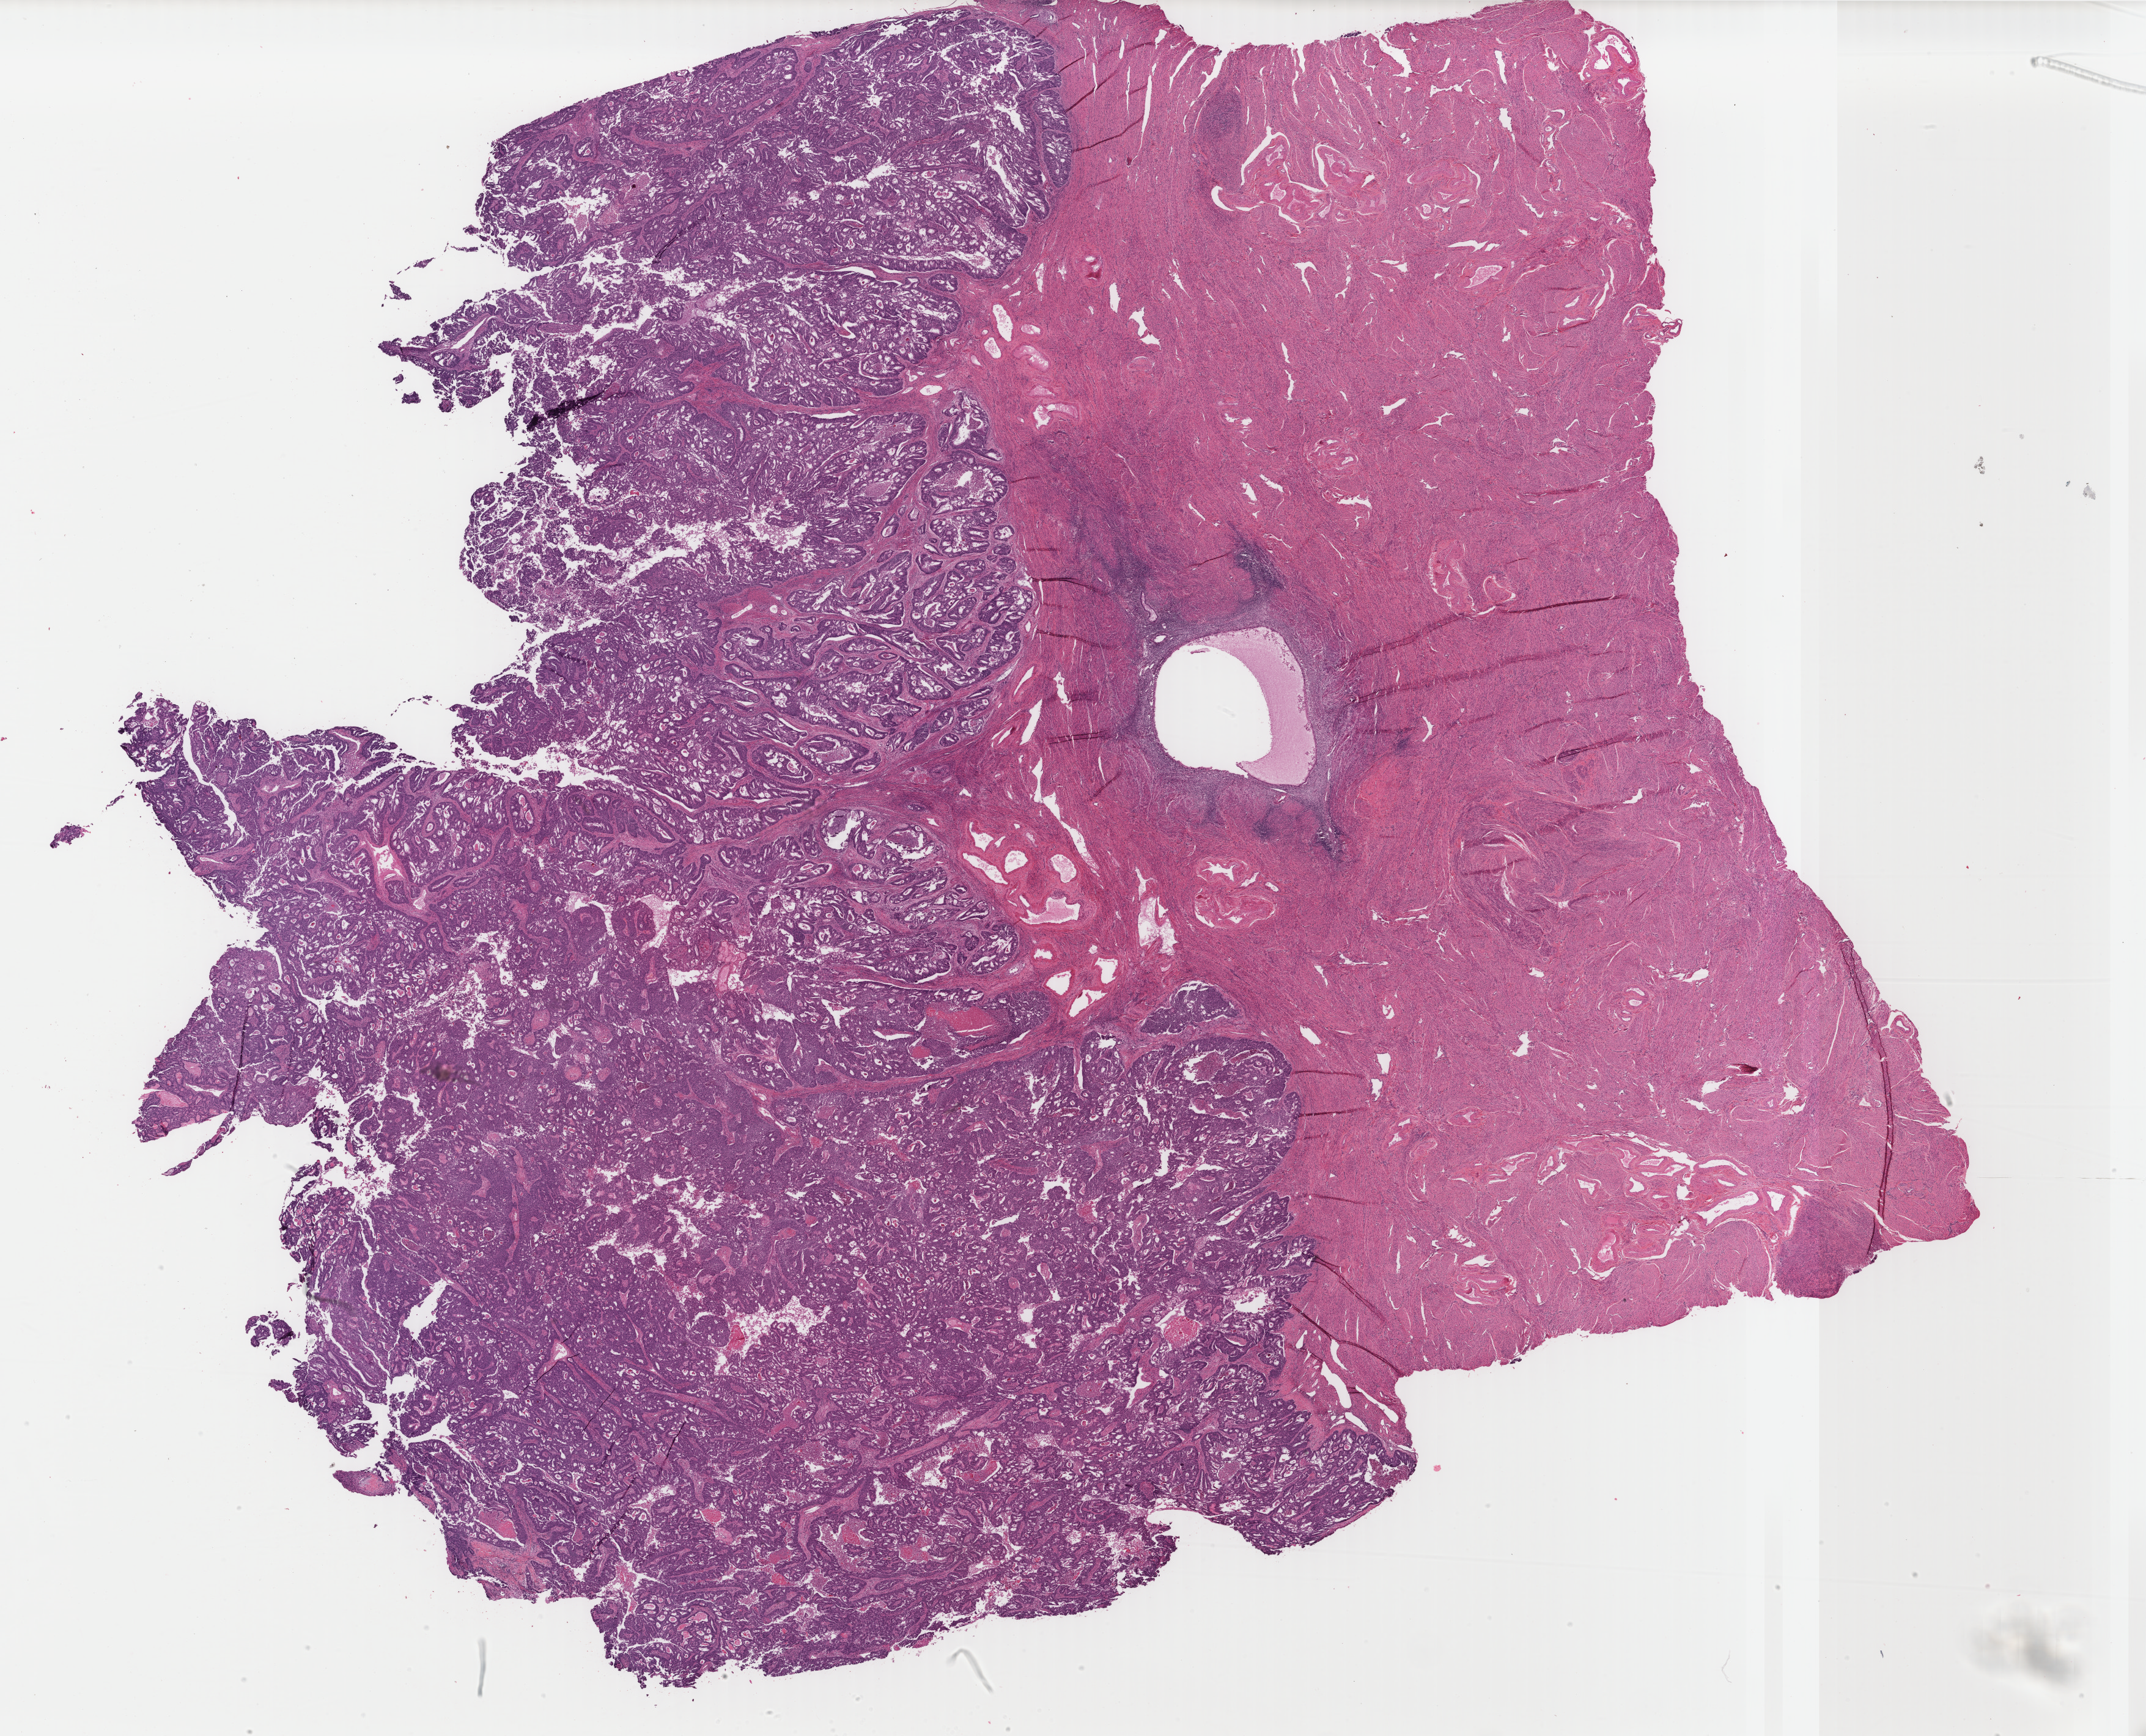
Whole-slide histology image, Hematoxylin and eosin (H&E) stained — a low-resolution overview of the entire scanned area, about 27.9 x 22.5 mm (slide scanned at 40x), formalin-fixed paraffin-embedded (FFPE) diagnostic section, primary tumour sample from the uterus. Female, age 58 years at initial diagnosis. Histologic grade: G2 (moderately differentiated).
FIGO stage: IB. Histologic diagnosis: Endometrioid adenocarcinoma, NOS (endometrium).